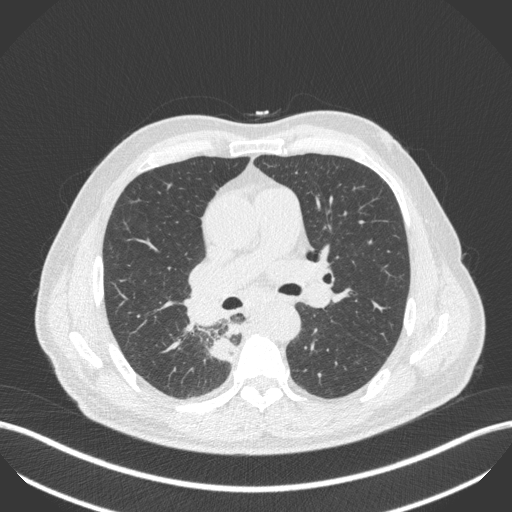
Chest CT, one axial slice; slice 274 of 451 in the series (ordered by position); 100 kVp; lung window (W 1500 / L -600 HU); 1 mm slice thickness; 512 × 512 image matrix. Patient: male, 61 years. From the clinical record (not read from this slice): clinical TNM (as recorded): T1 N0 M0; histopathological grade: G3.
Structures marked on this image (bounding box drawn by a radiologist):
- lung tumour (recorded histology: small cell carcinoma): bounding box <200,333,238,367> (left, top, right, bottom; pixels)